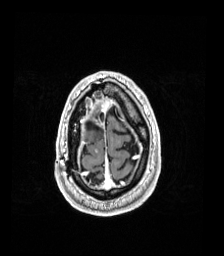
Brain MRI from a brain-tumour surgery series, one axial slice; position 28 of 192 along the scan axis; T1-weighted post-contrast; 1 mm slice thickness; 224 × 256 image matrix. From the clinical record (not read from this slice): histopathology: Astrocytoma; WHO grade: 4.
Outlined on this slice (expert manual segmentation):
- previous resection cavity: bounding box [x1, y1, x2, y2] px = [85, 121, 101, 131]